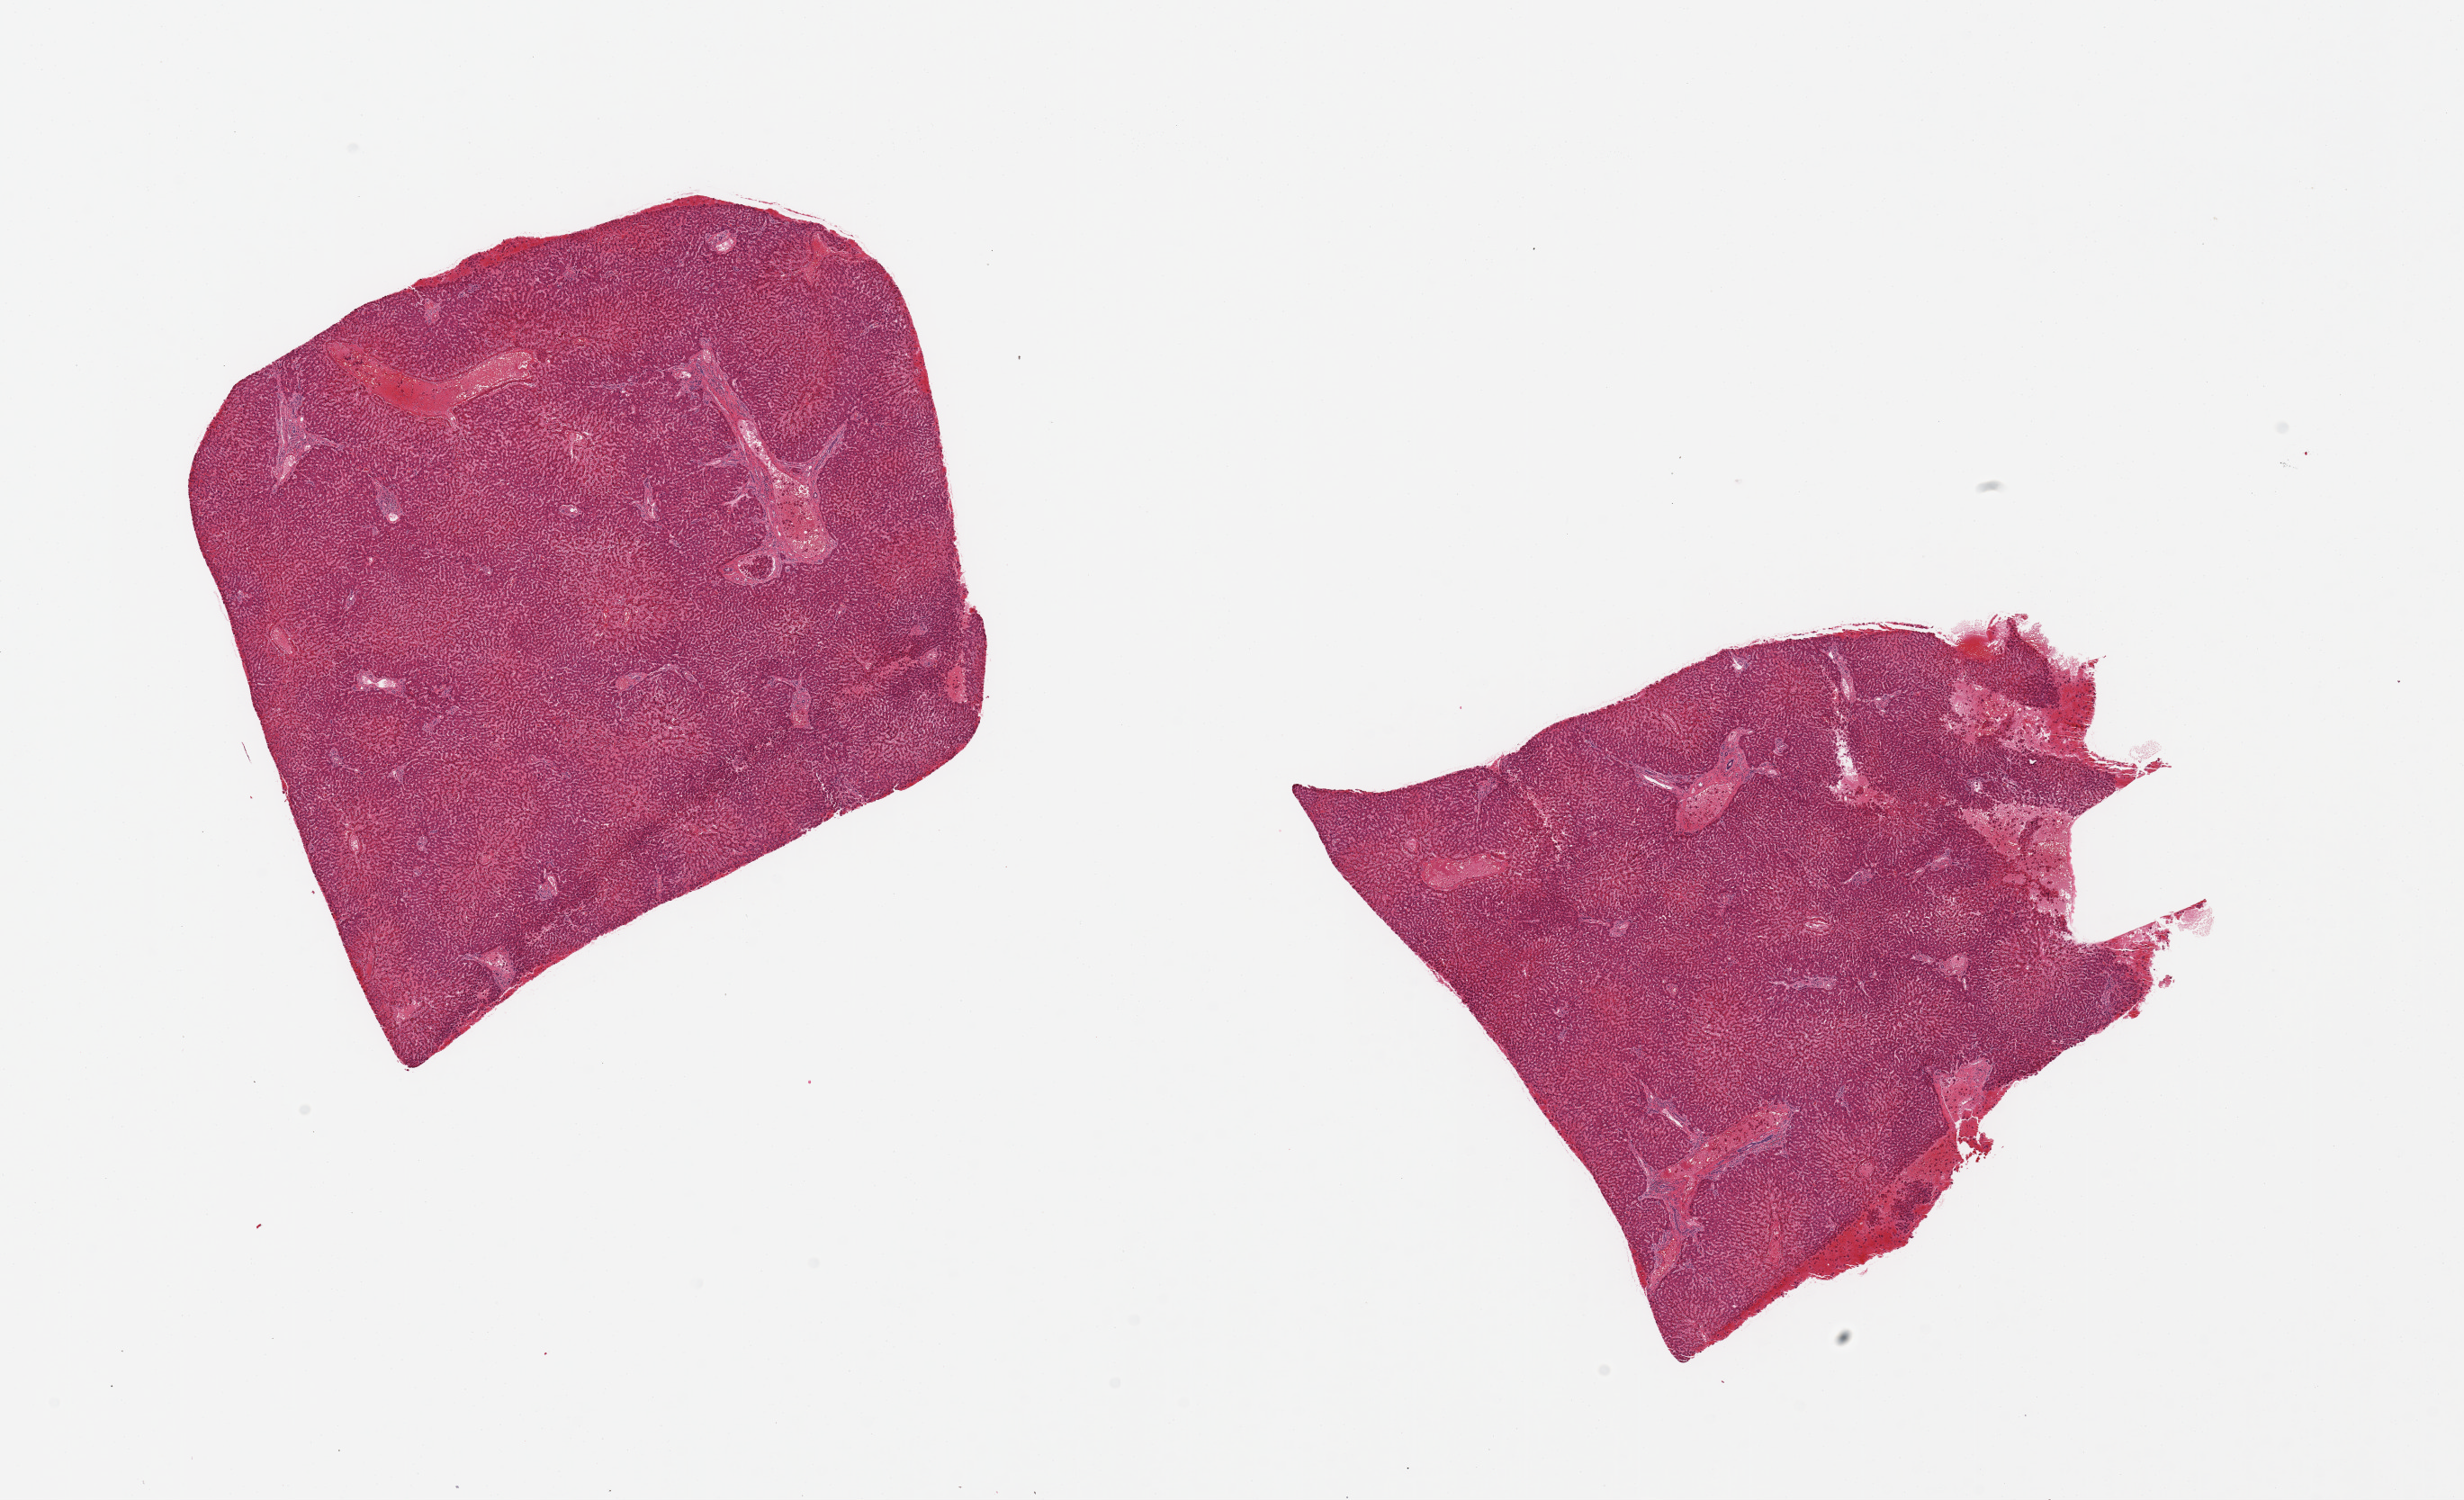
Hematoxylin and eosin (H&E) whole-slide image — whole scanned area (about 21.7 x 13.2 mm) shown as a low-resolution overview. PAXgene-fixed, paraffin-embedded tissue. Sampled site (target tissue): liver. Donor tissue sample. Donor sex: female.
Pathologist's review note for this sample: 2 pieces; central congestion.